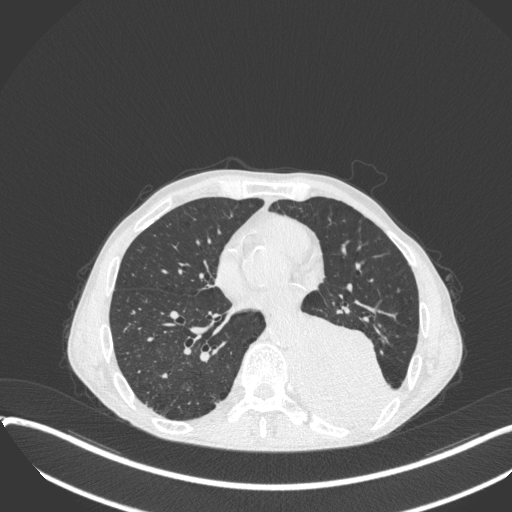
Chest CT, one axial slice; slice 153 of 400 in the series (ordered by position); lung window (W 1500 / L -600 HU); 512 × 512 image matrix. Male patient, age 57 years. From the clinical record (not read from this slice): clinical TNM (as recorded): T4 N0 M0.
Structures marked on this image (rectangle marked by the reading radiologist):
- lung tumour (recorded histology: squamous cell carcinoma): bounding box <294,309,393,433> (left, top, right, bottom; pixels)